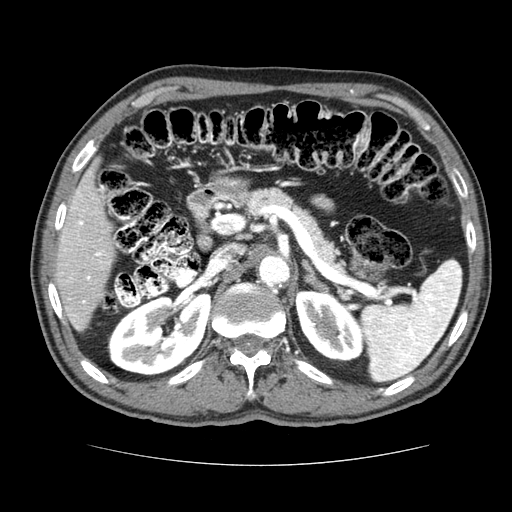
Contrast-enhanced abdominal CT (liver protocol), one axial slice. Slice 38 of 79 in the series (ordered by position). Reconstruction kernel STANDARD. 120 kVp. Soft-tissue window (W 400 / L 40 HU). 2.5 mm slice thickness. 512 × 512 image matrix, field of view 360 × 360 mm. From the clinical record (not read from this slice): diagnosis: hepatocellular carcinoma (patient treated with transarterial chemoembolisation; whether this scan precedes or follows treatment is not stated here); TNM stage (as recorded): Stage-I; Child-Pugh class: A; tumour nodularity: uninodular.
Annotated regions visible in this slice (semi-automatically segmented with operator editing):
- liver parenchyma outside the tumour (the mass and vessels are separate outlines, so this box may not span the whole liver): bounding box <54,166,114,332> (left, top, right, bottom; pixels)
- liver vessels: <64,192,102,328>